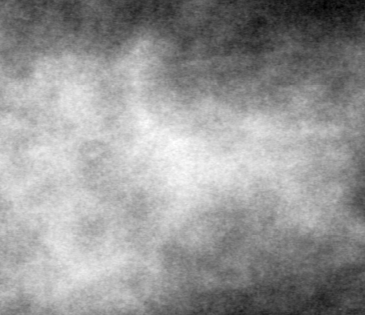
Region of interest cut from a scanned film mammogram (one marked finding), left breast, MLO view, BI-RADS breast density category 3 (scale 1–4).
- Finding: mass, shape oval, margins obscured / ill defined; BI-RADS assessment category 4; pathology (as recorded): benign.